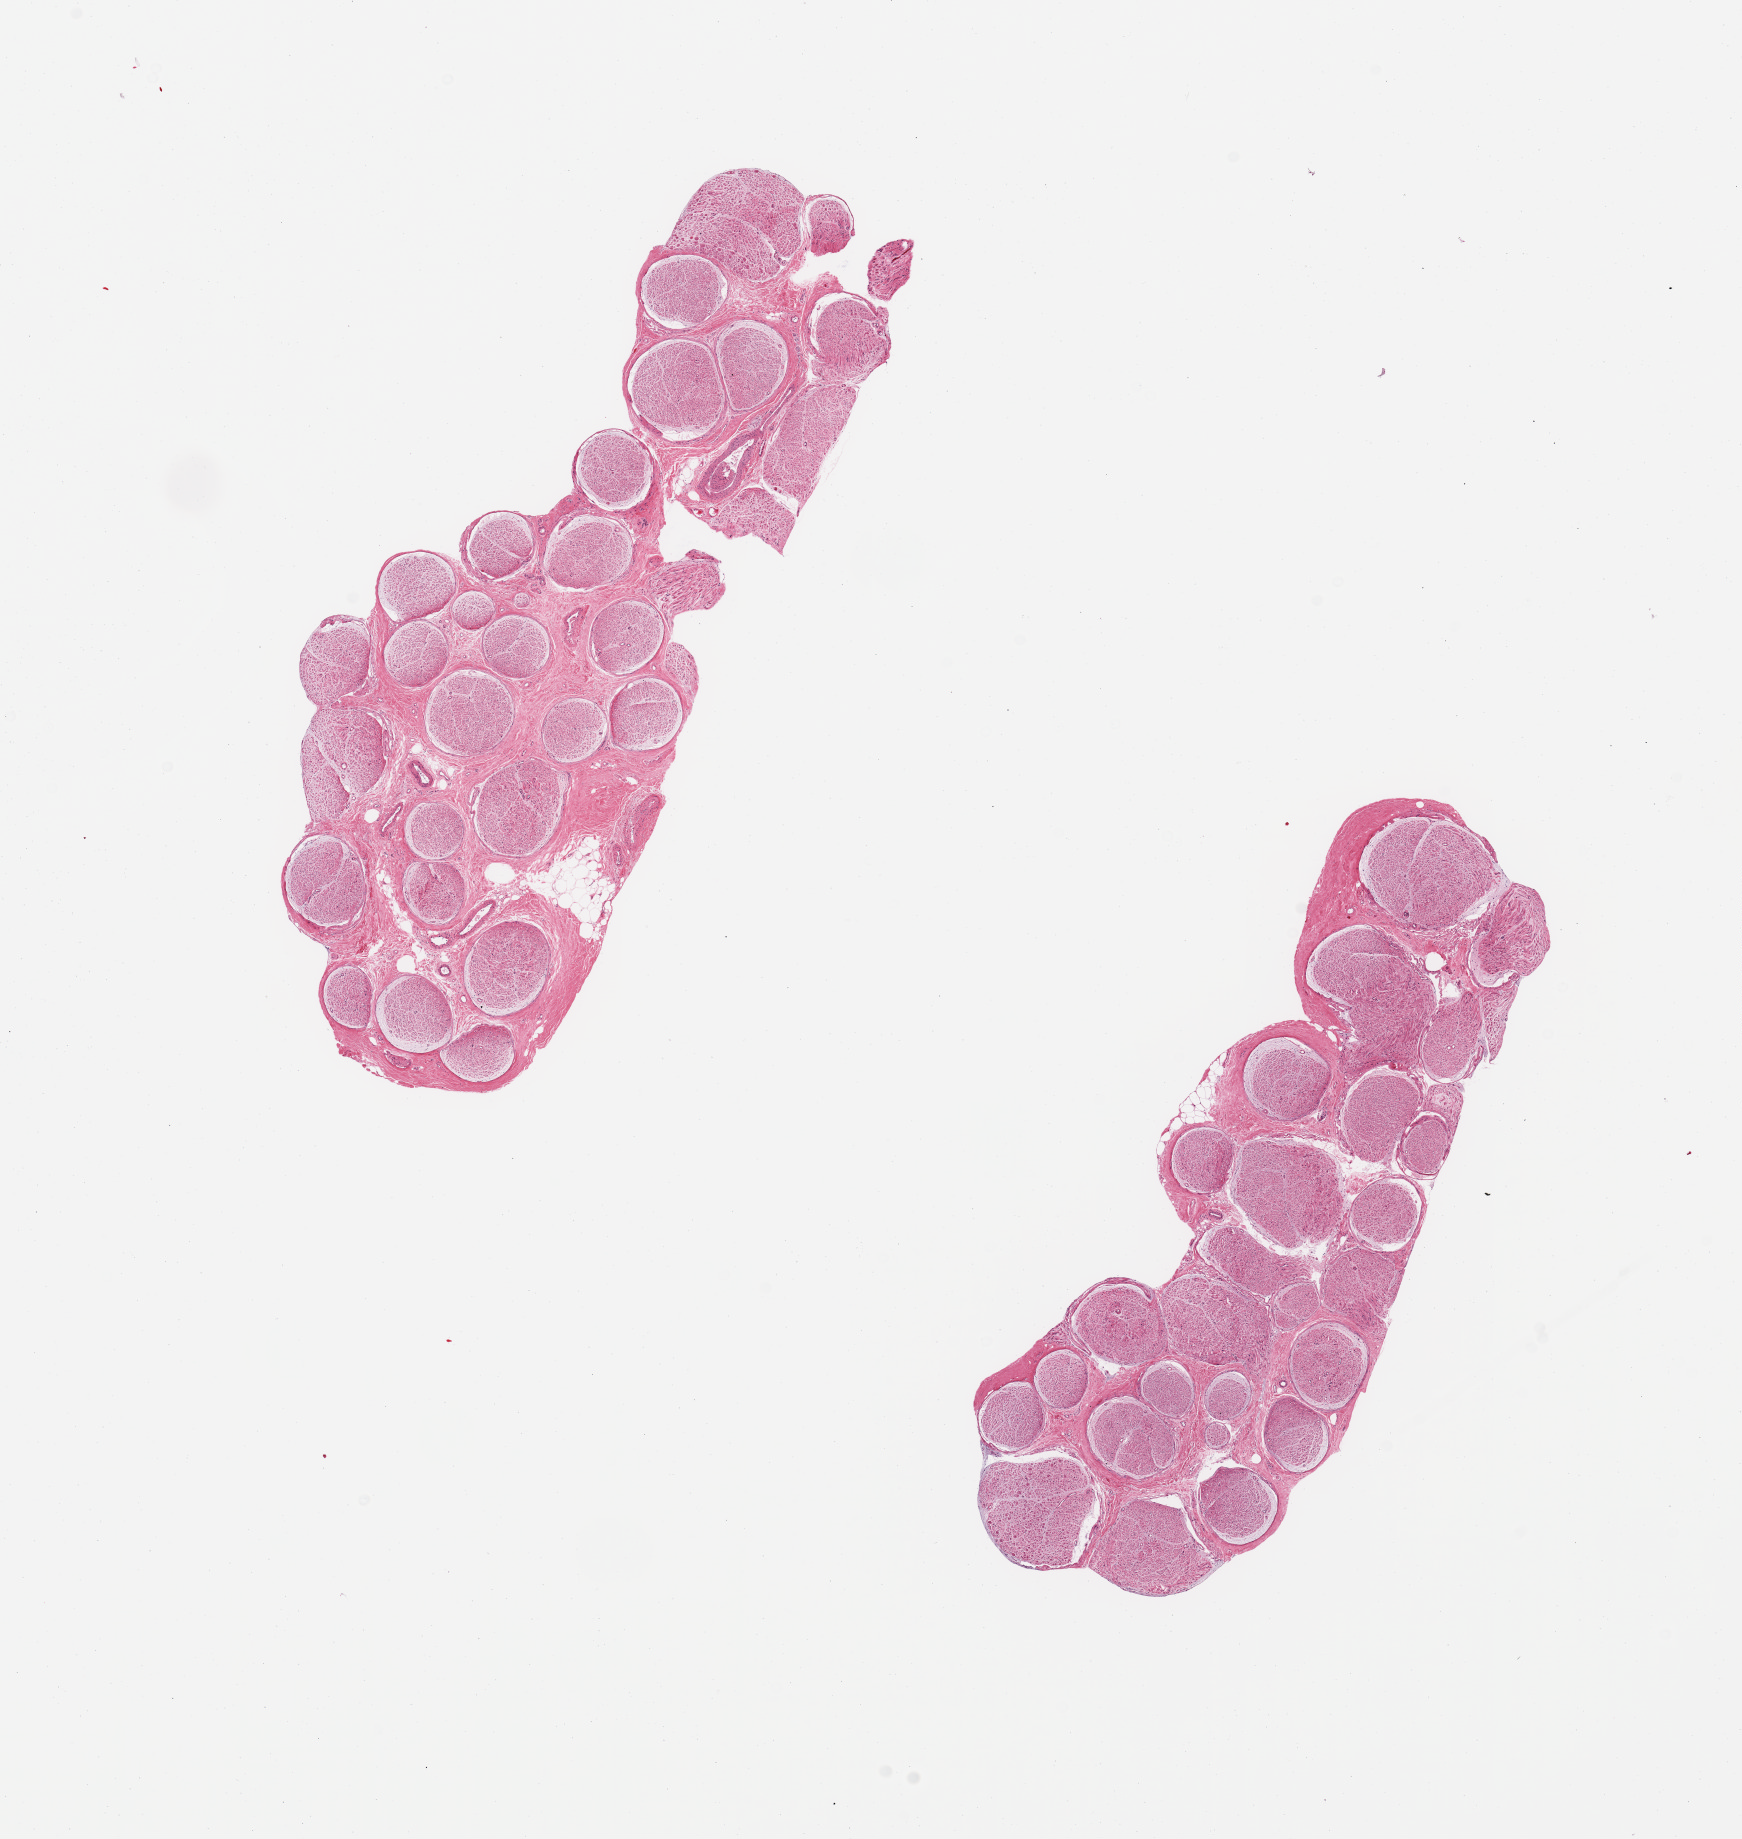
Whole-slide image, H&E stain — a low-resolution overview of the entire scanned area, about 13.8 x 14.5 mm (slide scanned at 20x); PAXgene-fixed, paraffin-embedded tissue; section of tibial nerve (target tissue); donor tissue sample. Donor: male.
• pathologist's review note for this sample: 2 pieces; nerve with prineurium and insignificant internal fat